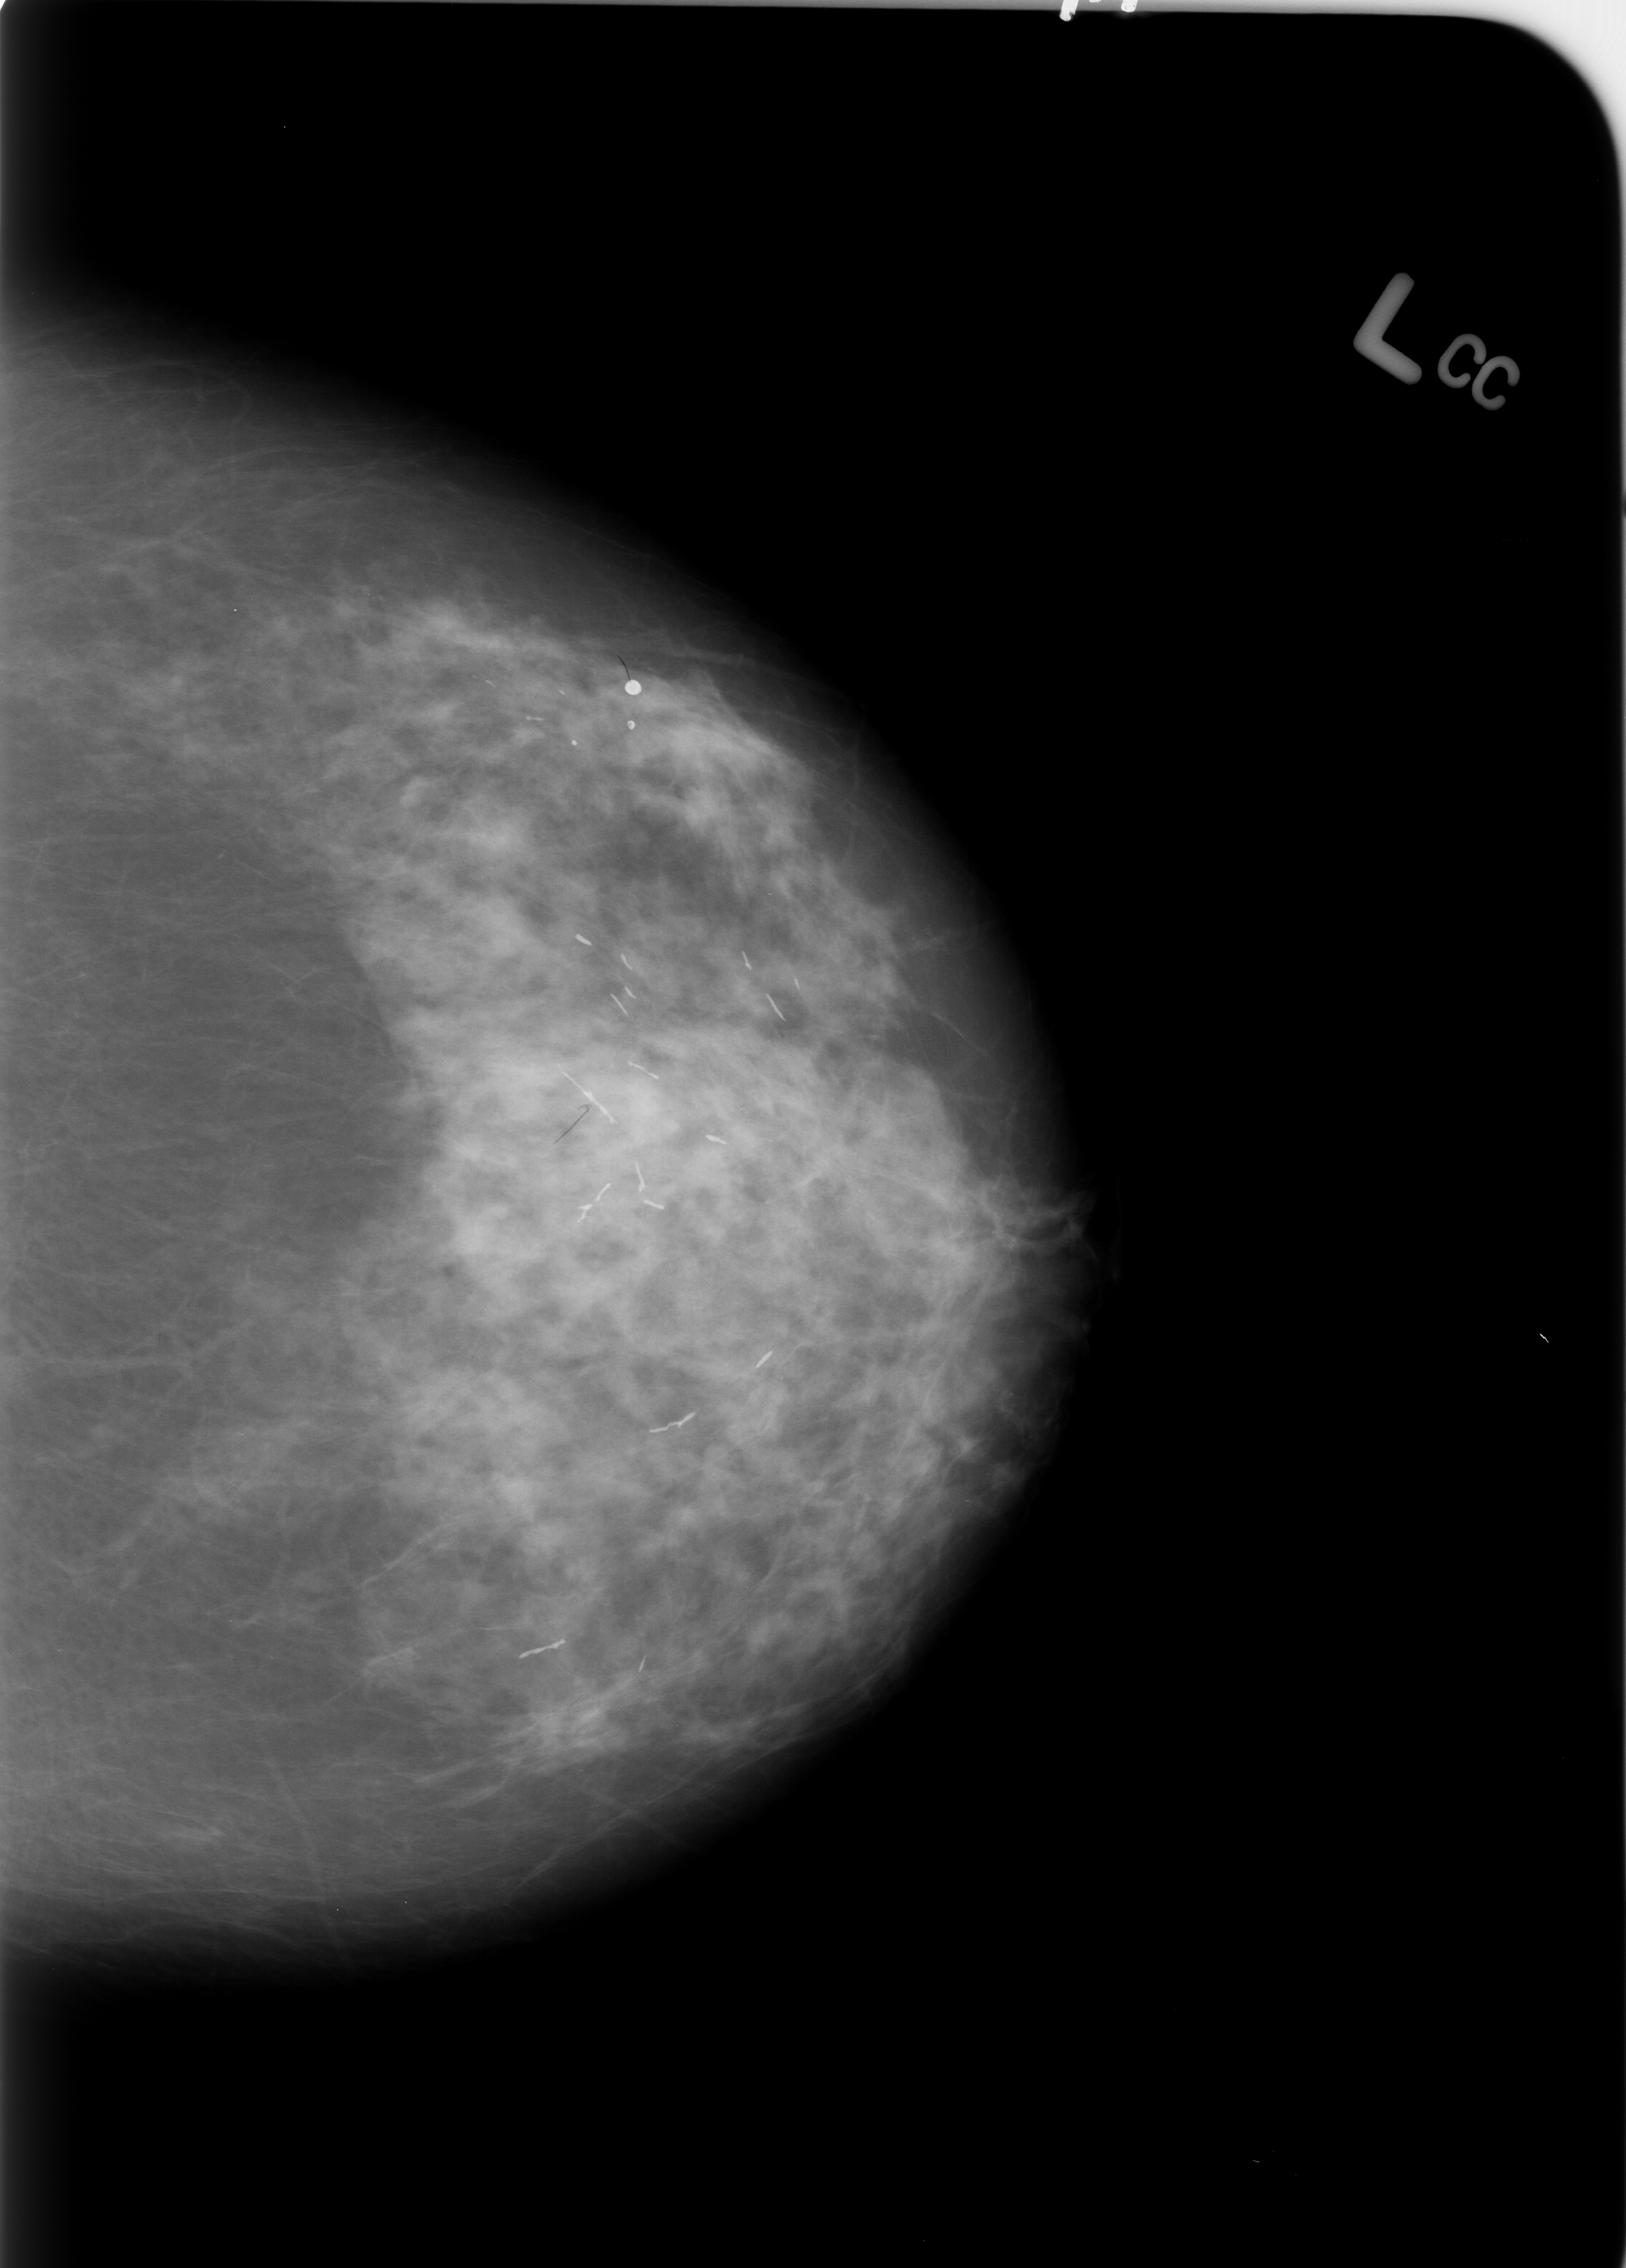
Digitized screen-film mammogram; left breast; CC view; BI-RADS breast density category 3 (scale 1–4).
Radiologist-marked abnormalities on this image: Finding 1 of 6: calcifications, morphology large rodlike / round and regular, distribution regional; BI-RADS assessment category 2; benign without callback (not worked up further). Finding 2 of 6: calcifications, morphology large rodlike / round and regular, distribution regional; BI-RADS assessment category 2; benign; no additional work-up was recommended (benign without callback). Finding 3 of 6: calcifications, morphology large rodlike / round and regular, distribution regional; BI-RADS assessment category 2; benign; no additional work-up was recommended (benign without callback). Finding 4 of 6: calcifications, morphology large rodlike / round and regular, distribution regional; BI-RADS assessment category 2; benign; no additional work-up was recommended (benign without callback). Finding 5 of 6: calcifications, morphology large rodlike / round and regular, distribution regional; BI-RADS assessment category 2; benign; no additional work-up was recommended (benign without callback). Finding 6 of 6: calcifications, morphology large rodlike / round and regular, distribution regional; BI-RADS assessment category 2; benign; no additional work-up was recommended (benign without callback).